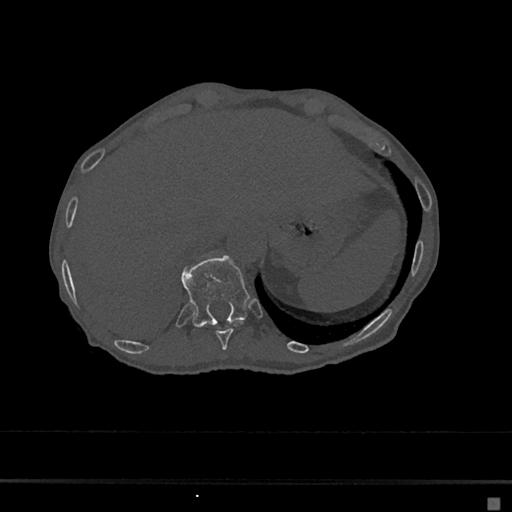
CT including the spine, one axial slice. Position 190 of 797 along the scan axis. Reconstruction kernel Br40s/3. 120 kVp. Bone window (W 1800 / L 400 HU). 0.5 mm slice thickness. 512 × 512 image matrix, field of view 360 × 360 mm. Female patient, age 68 years. Case-level facts recorded for this patient, not image findings: primary cancer: renal.
Outlined on this slice (semi-automatic segmentation, software-assisted and operator-edited):
- T10 vertebra: bounding box [x1, y1, x2, y2] px = [215, 321, 244, 350]
- T11 vertebra: [182, 256, 250, 327]